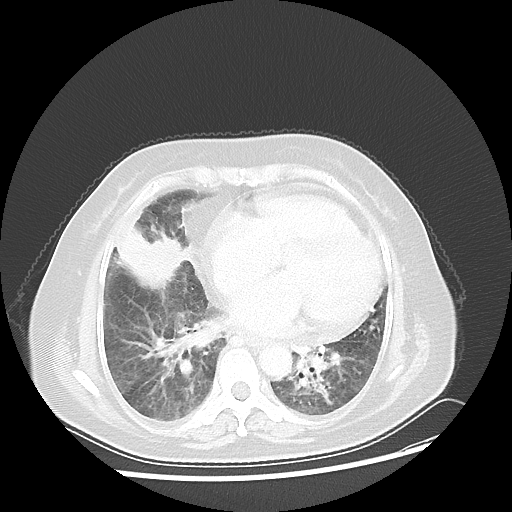
Chest CT, one axial slice. Position 18 of 45 along the scan axis. 100 kVp. Lung window (W 1500 / L -600 HU). 5 mm slice thickness. 512 × 512 image matrix. Patient: female, 67 years. Case-level facts recorded for this patient, not image findings: clinical TNM (as recorded): T2a N3 M1a.
Outlined on this slice (bounding box drawn by a radiologist):
- lung tumour (recorded histology: adenocarcinoma): bounding box <119,224,187,292> (left, top, right, bottom; pixels)